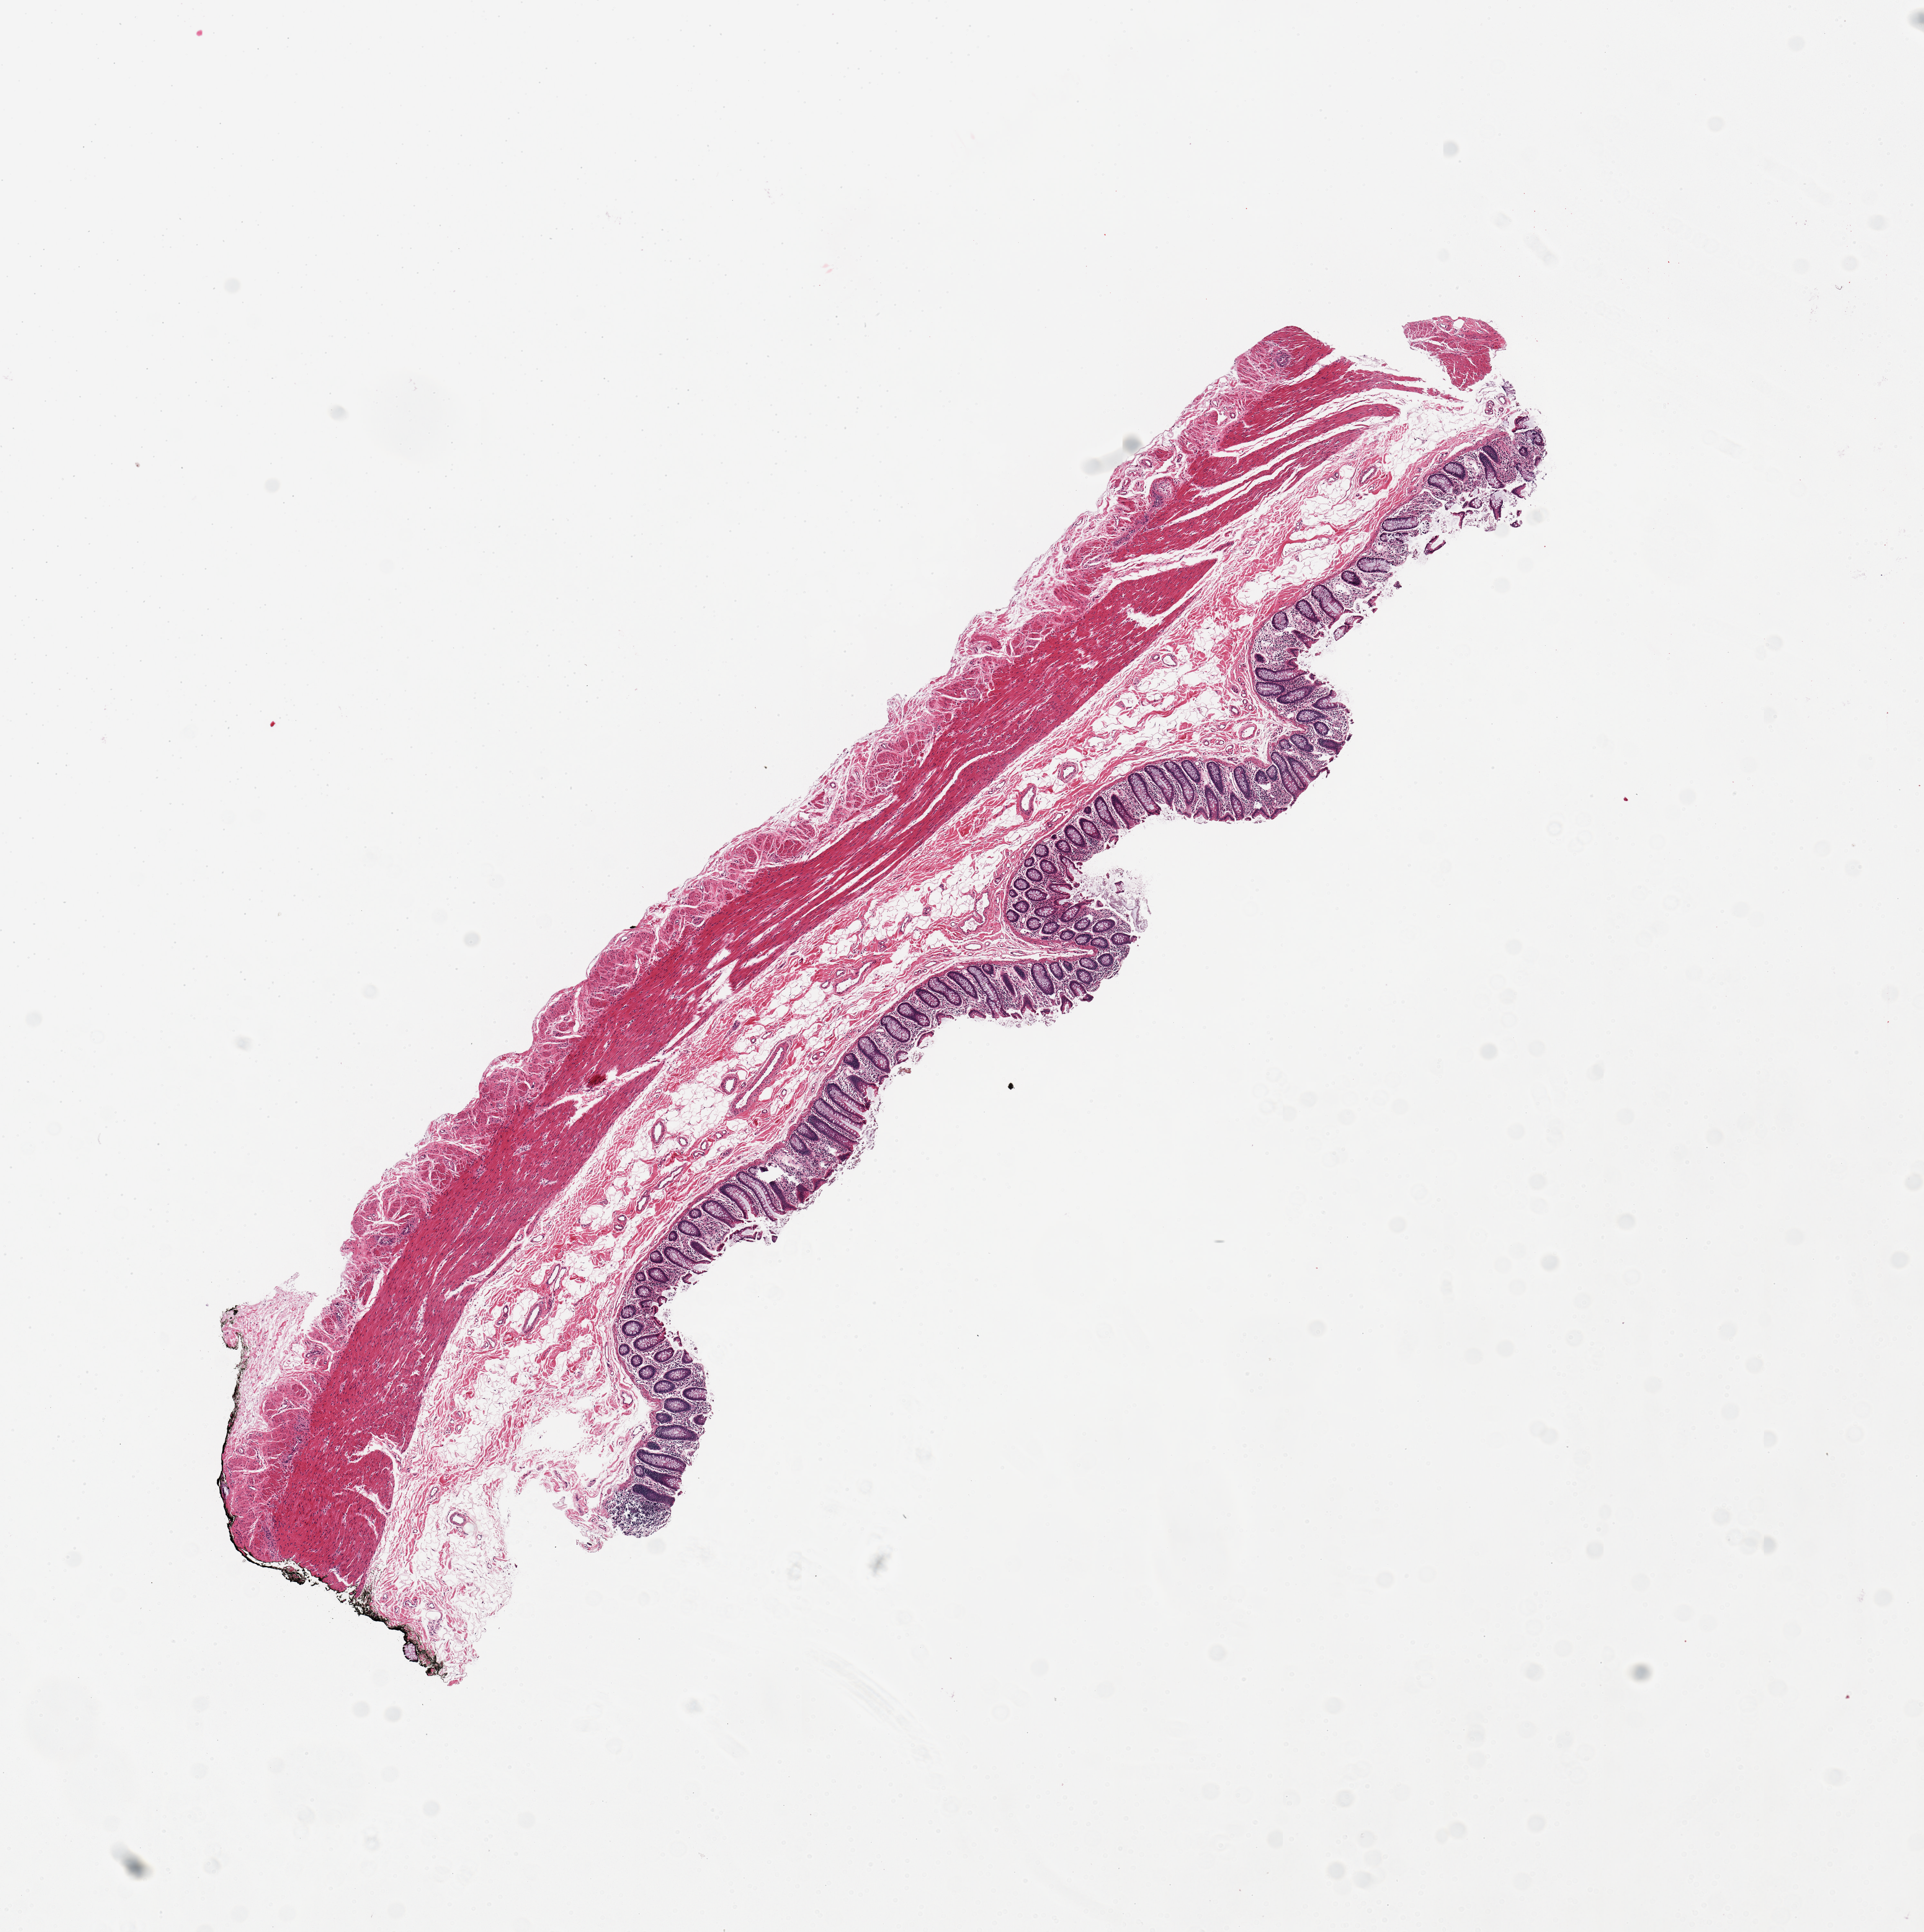
Hematoxylin and eosin (H&E) whole-slide image, brightfield — low-resolution overview of the scanned area, about 11.8 x 11.9 mm. PAXgene-fixed paraffin-embedded (PFPE) section. Target tissue: transverse colon. Donor tissue sample. Donor sex: male.
Pathologist's review note for this sample: 1 piece; comparable to 25 block.